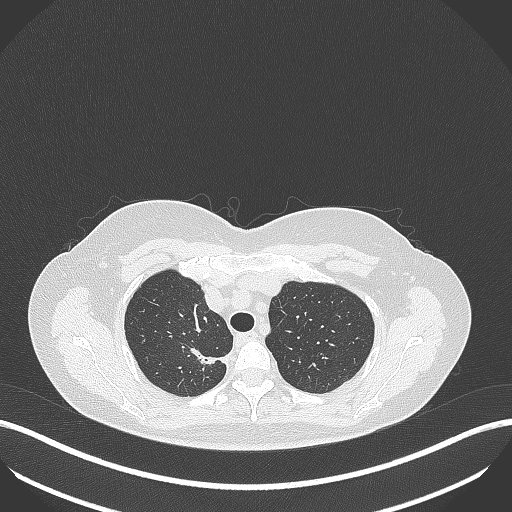
Chest CT, one axial slice. Slice 318 of 386 in the series (ordered by position). Reconstruction kernel B70f. 120 kVp. Lung window (W 1500 / L -600 HU). 1 mm slice thickness. 512 × 512 image matrix, field of view 400 × 400 mm. Patient: female, 65 years. Case-level facts recorded for this patient, not image findings: clinical TNM (as recorded): T1b N0 M0.
Structures marked on this image (bounding box drawn by a radiologist):
- lung tumour (recorded histology: adenocarcinoma): box from (x=187, y=342) to (x=231, y=372) px